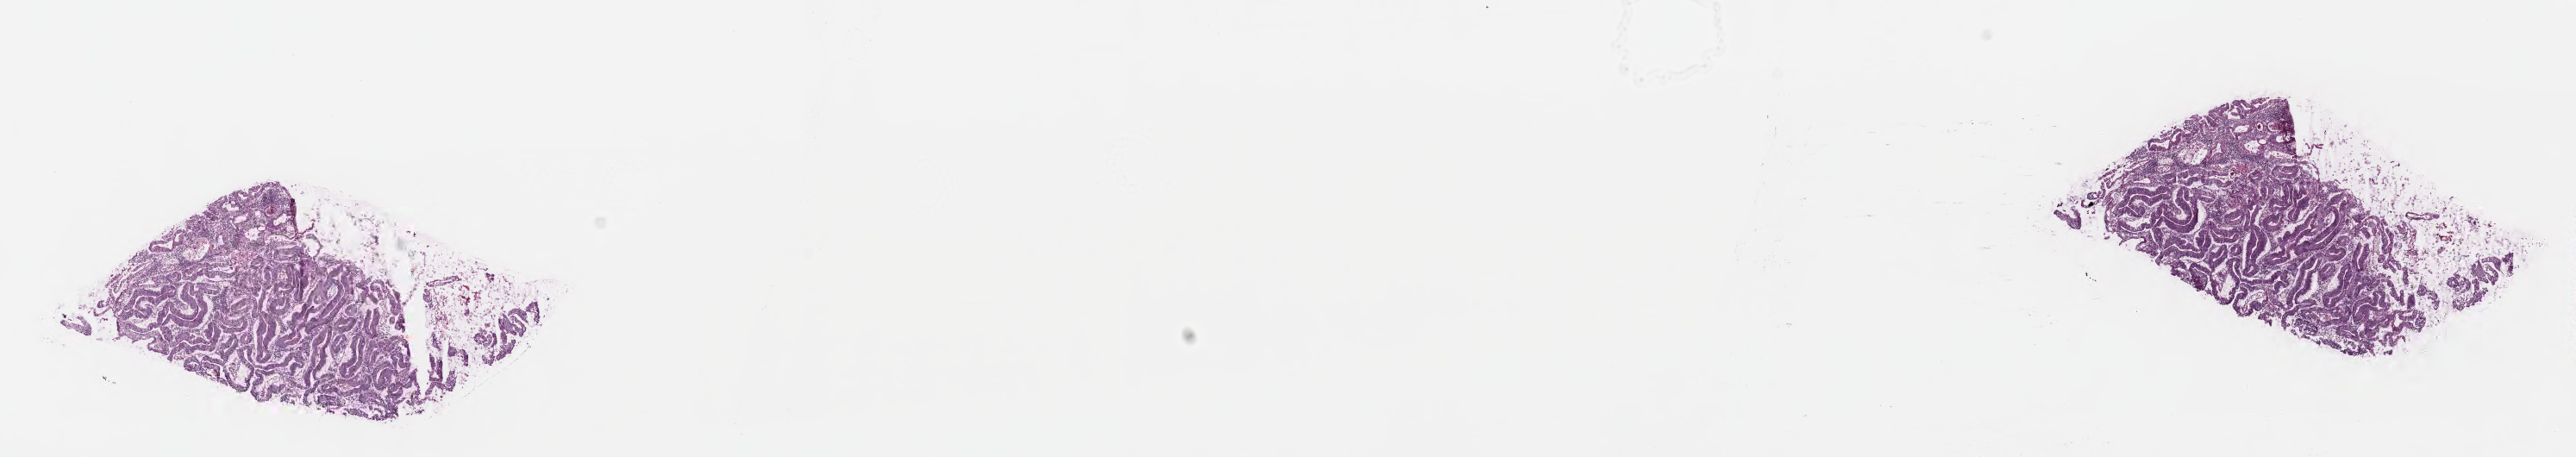
Whole-slide image, haematoxylin and eosin stain — whole scanned area (about 24.1 x 4.3 mm) shown as a low-resolution overview, frozen section (tissue freezing medium), specimen: primary tumor, anatomic site: ascending colon. Female, age 60 years at initial diagnosis. Tumor grade: GB (borderline). Slide review estimates, as recorded: tumor cells 85%, tumor nuclei 85%, stromal cells 2%, necrosis 0%, normal cells 13%. Inflammatory infiltration, as recorded: lymphocyte infiltration 10%, monocyte infiltration 1%, neutrophil infiltration 2%.
- histologic diagnosis: Adenocarcinoma, NOS
- AJCC pathologic stage: Stage IIIA
- section: bottom of the tissue portion